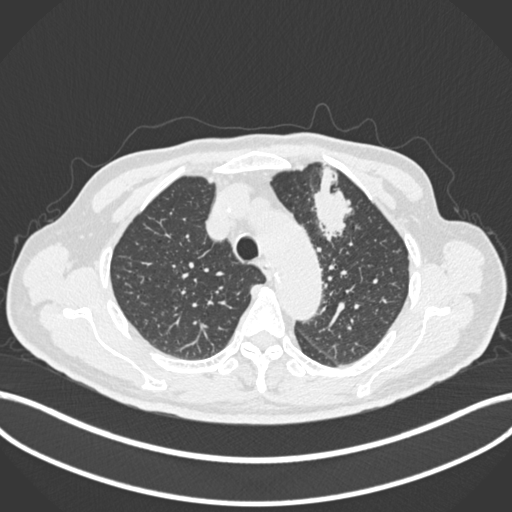
Chest CT, one axial slice. Position 196 of 261 along the scan axis. Reconstruction kernel B30f. Lung window (W 1500 / L -600 HU). 1 mm slice thickness. 512 × 512 image matrix. Male patient, age 74 years. Case-level facts recorded for this patient, not image findings: clinical TNM (as recorded): T2b N0 M1c.
Annotated regions visible in this slice (rectangle marked by the reading radiologist):
- lung tumour (recorded histology: adenocarcinoma): box from (x=305, y=158) to (x=361, y=246) px